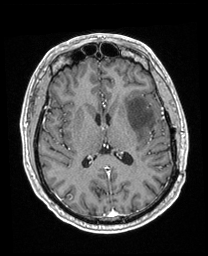
Brain MRI from a brain-tumour surgery series, one axial slice; position 102 of 208 along the scan axis; T1-weighted post-contrast; 208 × 256 image matrix. Case-level facts recorded for this patient, not image findings: histopathology: Astrocytoma; WHO grade: 3; IDH mutation: yes; tumour location: Left Insular.
Outlined on this slice (outlined manually by an expert reader):
- previous resection cavity: bounding box (x1, y1, x2, y2) in pixels: (152, 131, 154, 136)